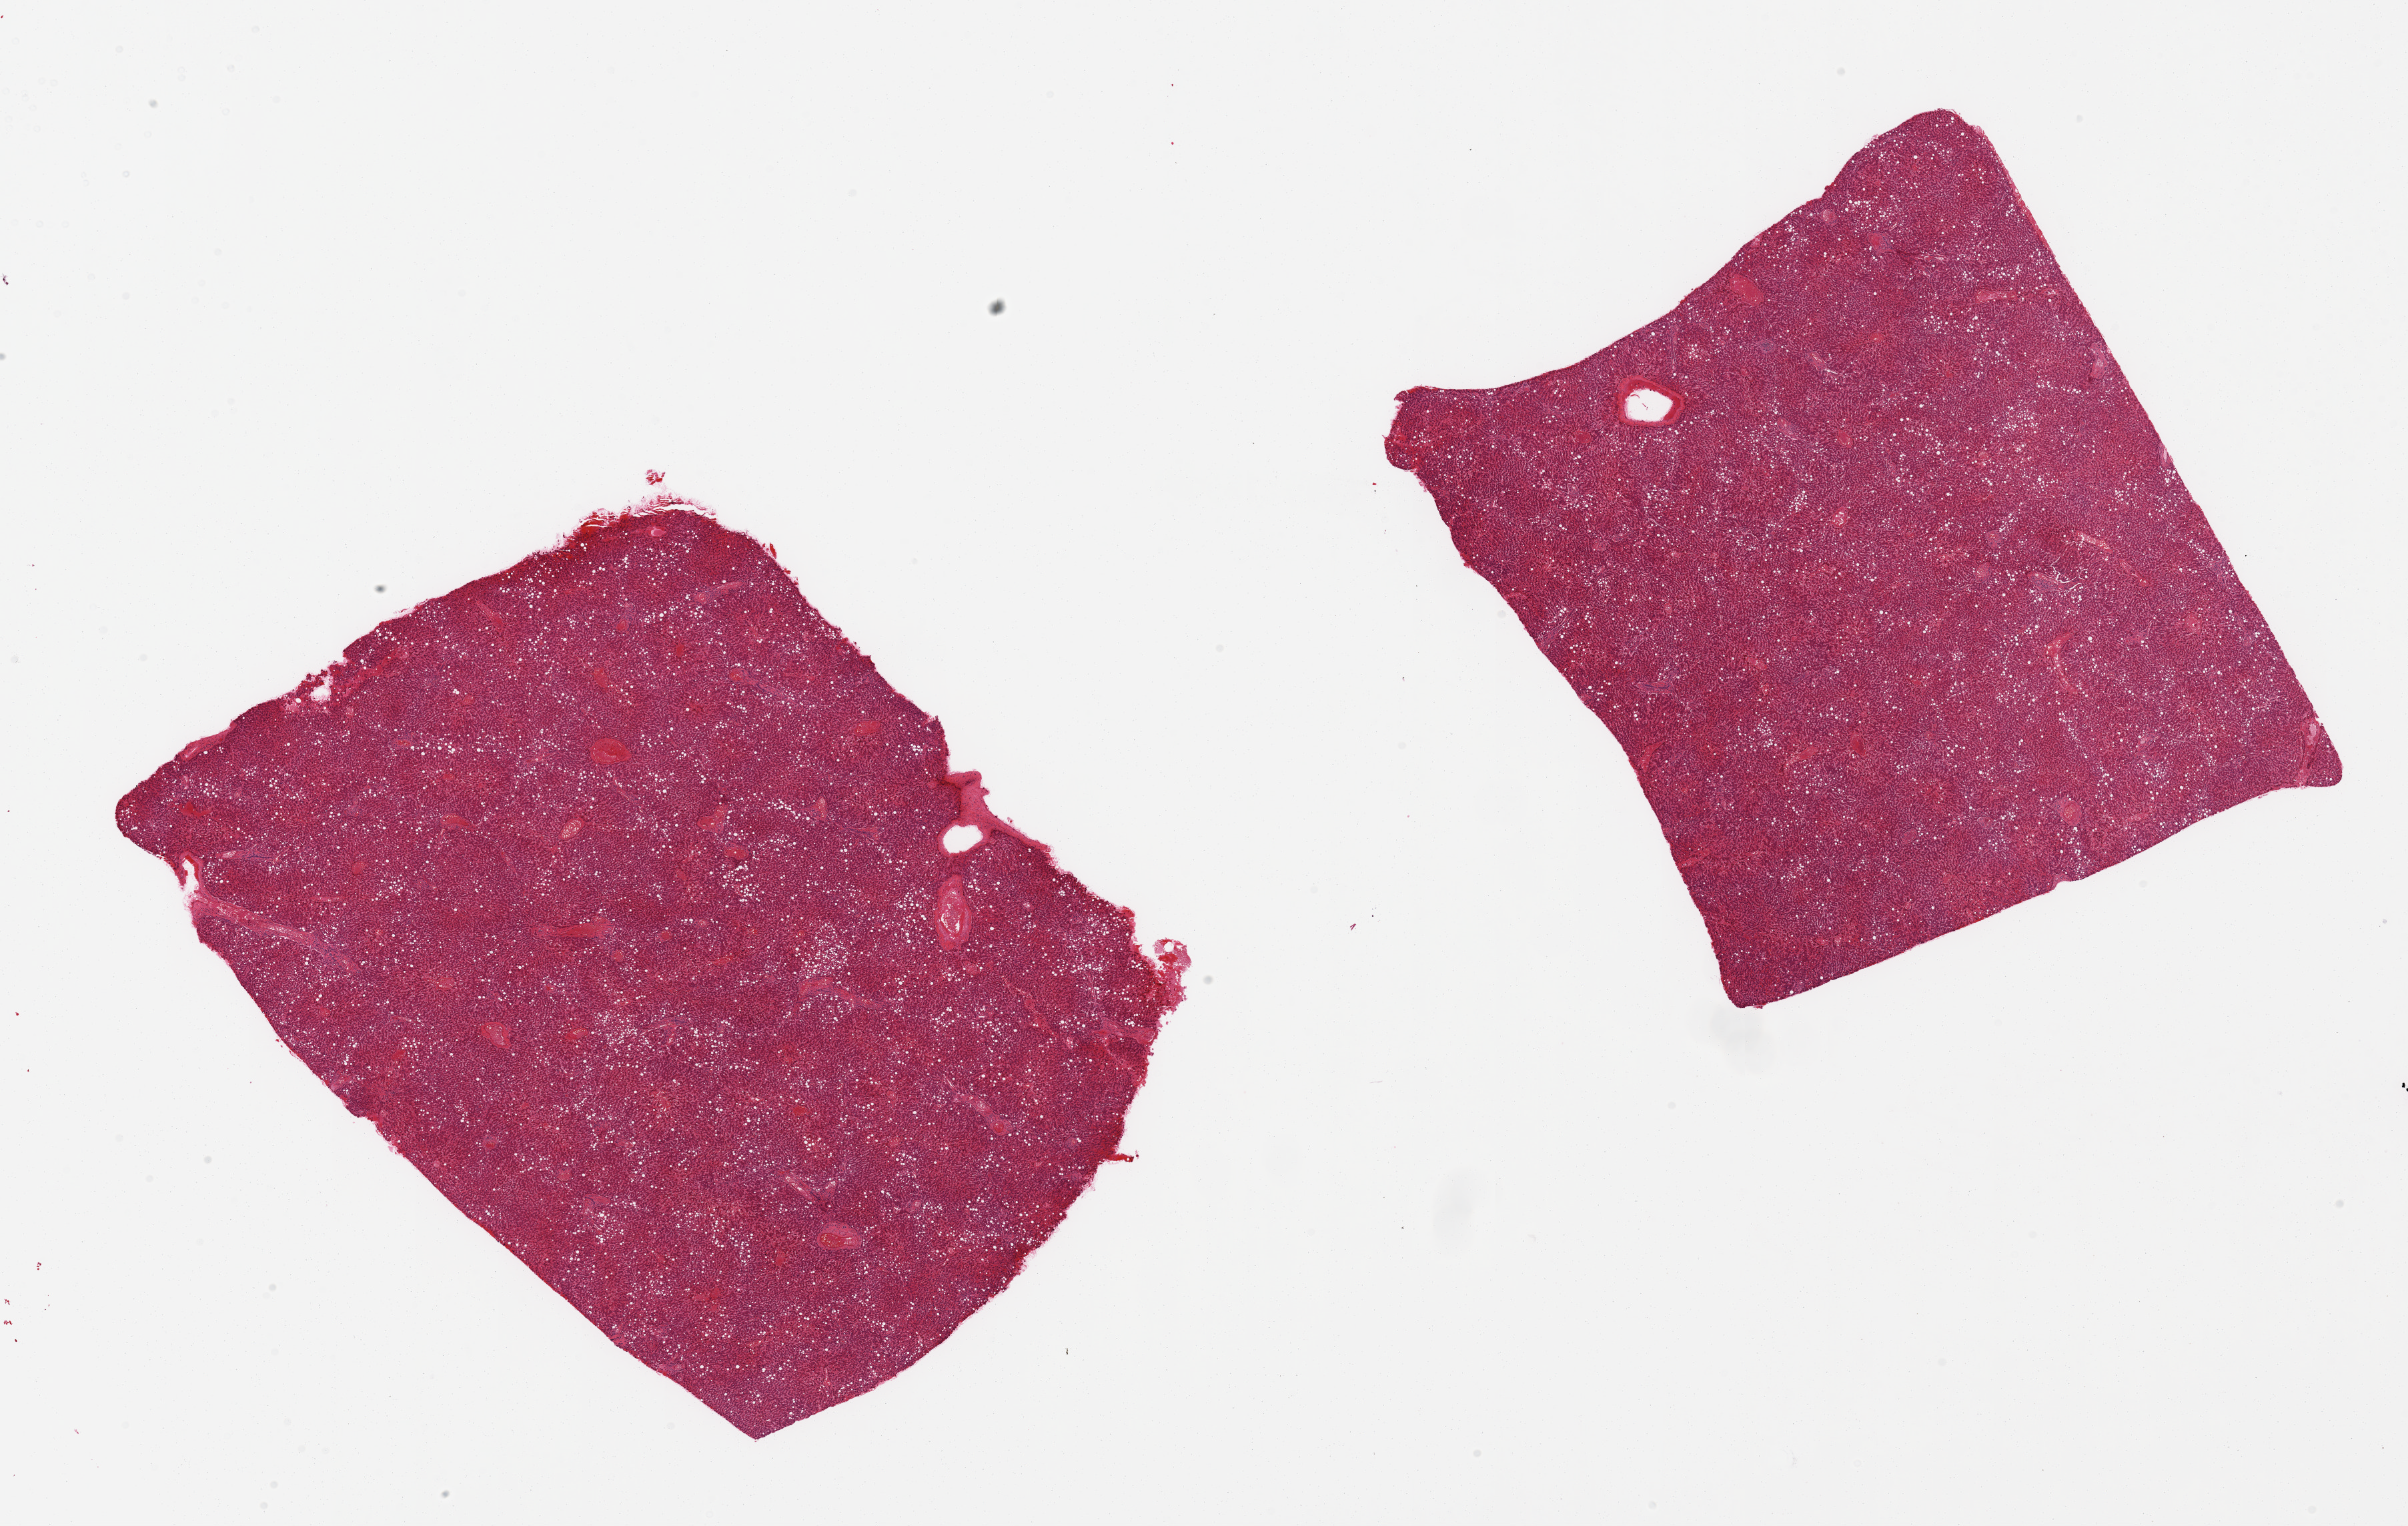
Whole-slide image, hematoxylin and eosin (H&E) stain, brightfield — shown as a low-resolution overview of the whole scanned area (about 28.5 x 18.1 mm, slide scanned at 20x), PAXgene-fixed paraffin-embedded (PFPE) section, section of liver (target tissue), donor tissue sample. Donor: female.
Review note (as recorded): 2 pieces, mild steatosis and passive congestion.